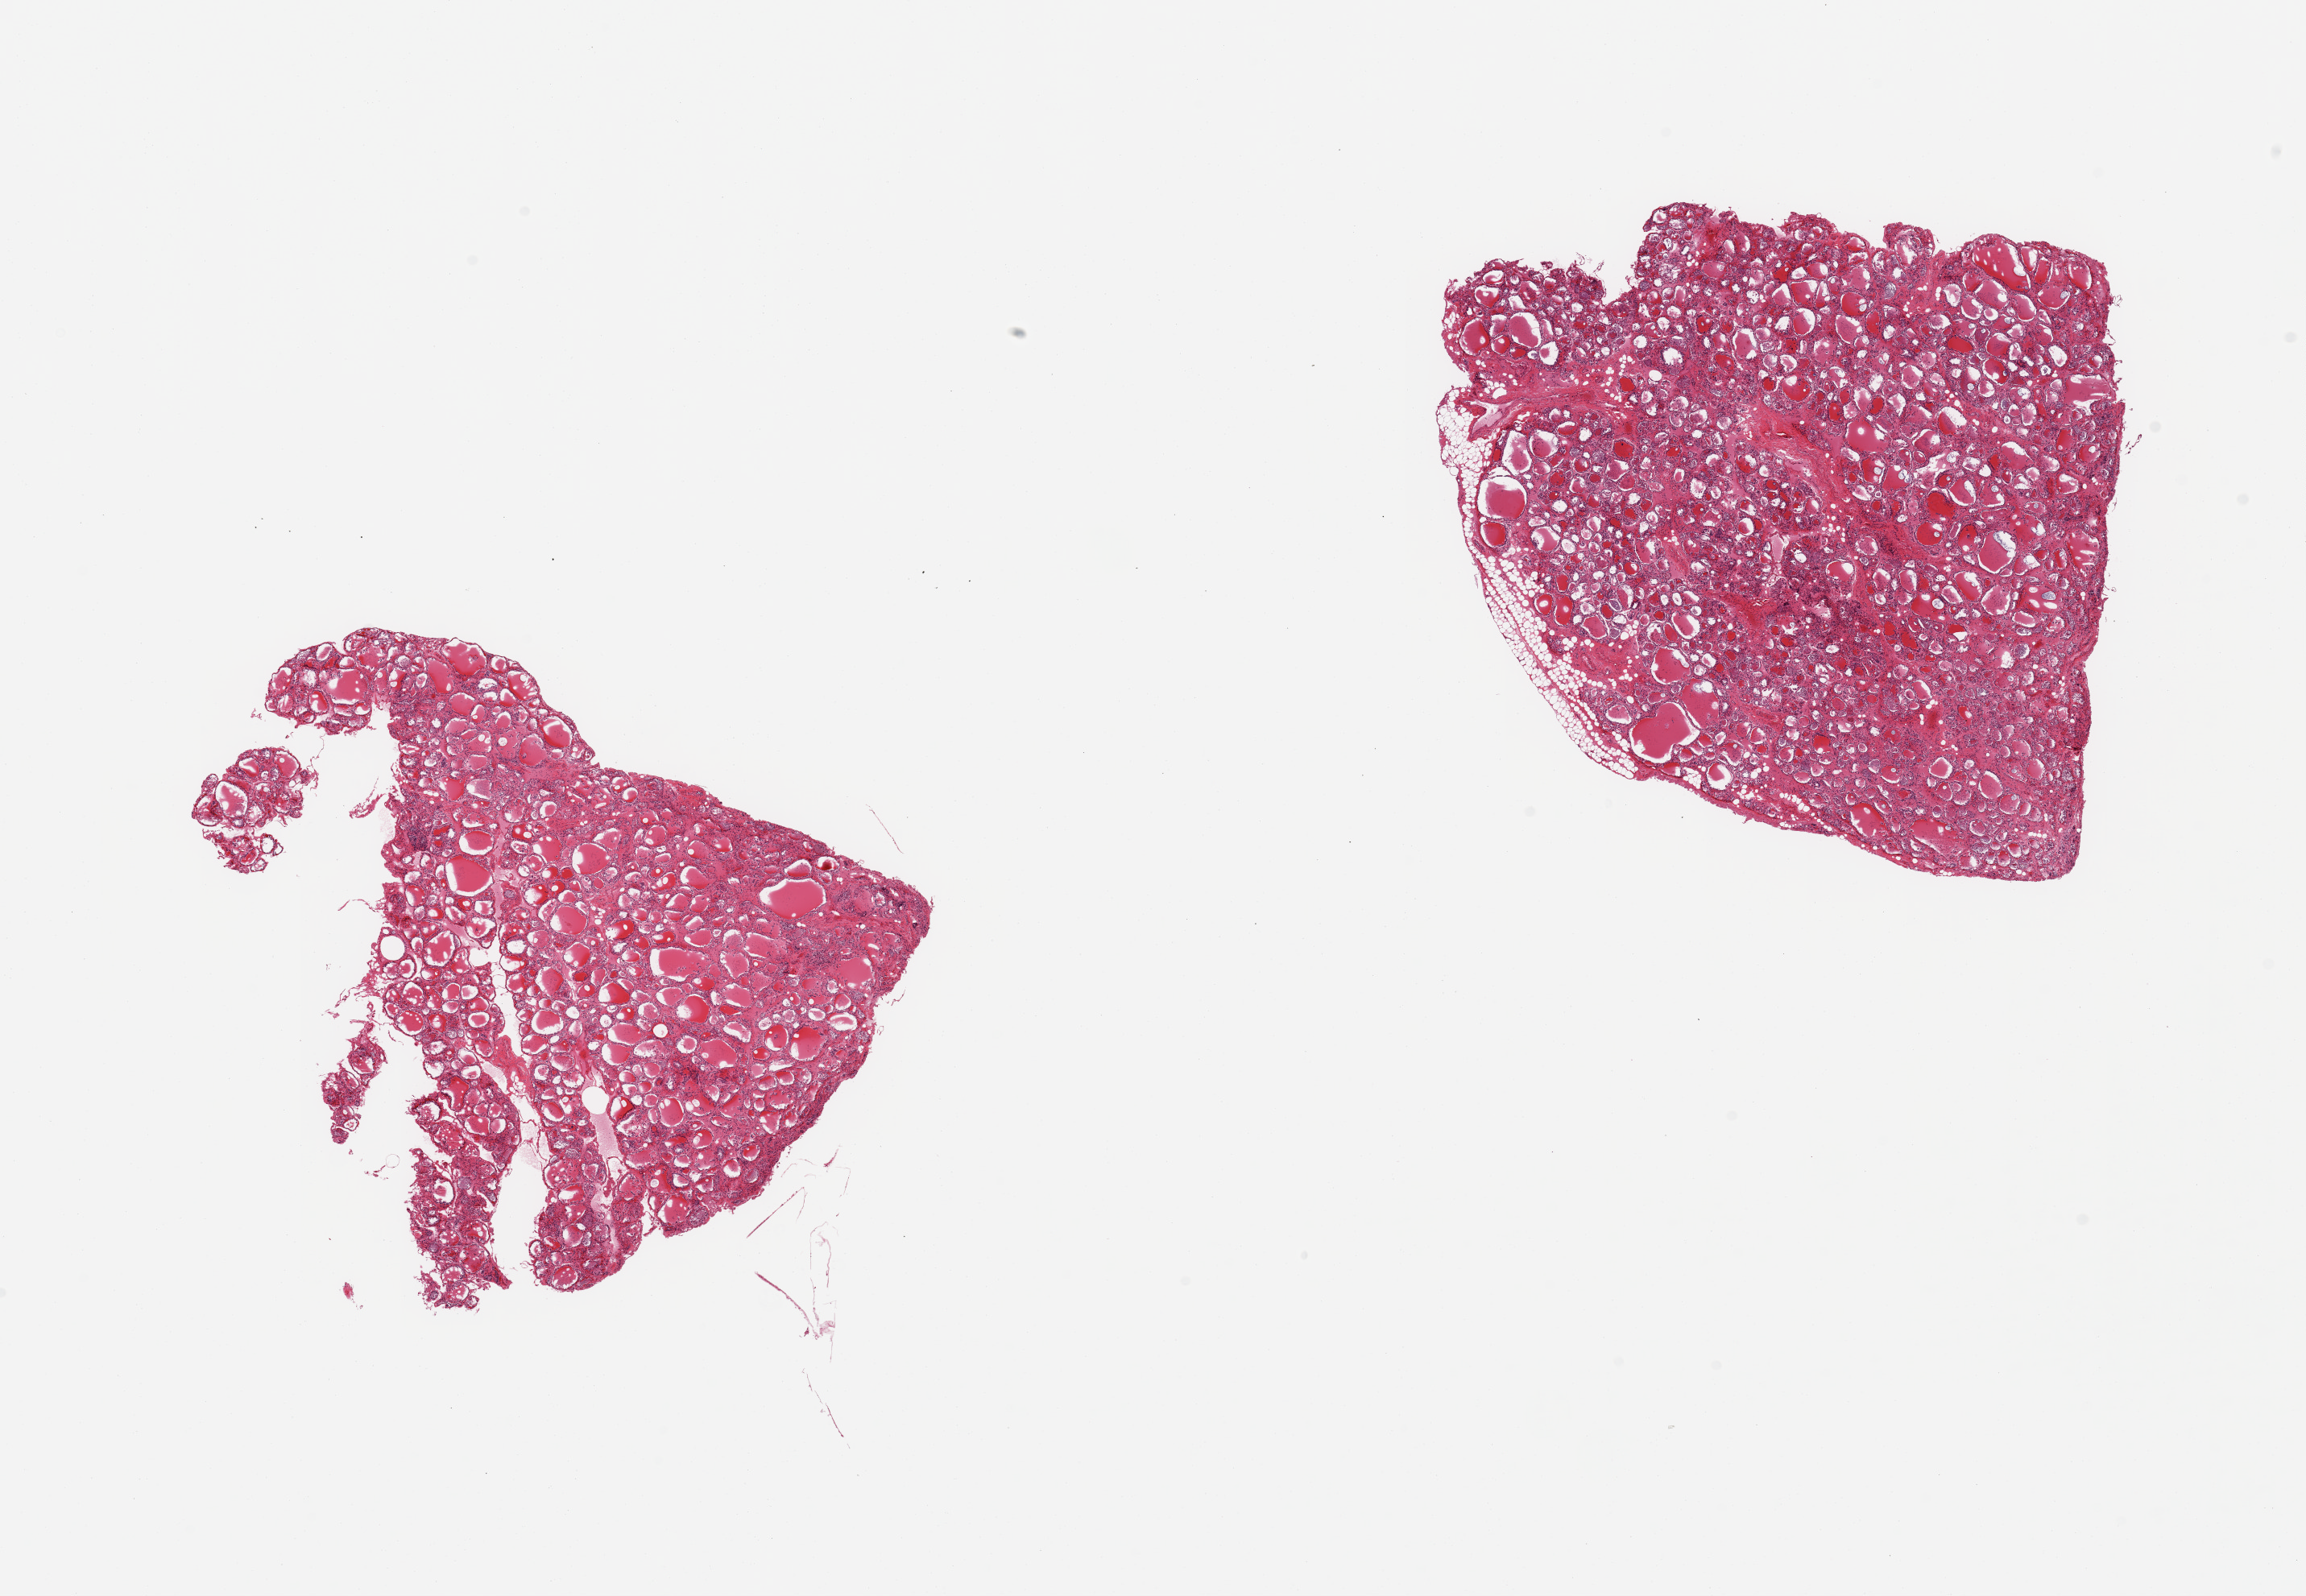
Digitized haematoxylin and eosin-stained section, brightfield — a low-resolution overview of the entire scanned area, about 22.6 x 15.7 mm (acquisition: 20x scan). PAXgene-fixed paraffin-embedded (PFPE) section. Target tissue: thyroid. Tissue donor sample. Male donor.
* review note (as recorded): 2 pieces; interstitial fibrosis